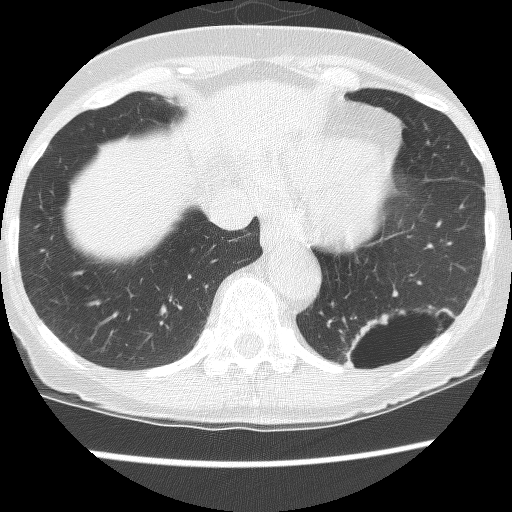
Axial slice from a low-dose chest CT screening exam, third annual screen, lung window (W 1500 / L -600 HU), 2.5 mm slice thickness, 120 kVp, 512 × 512 image matrix. Female, age 61 years at enrolment. Current smoker at enrolment.
- Expert reader's lesion annotation, bounding box (x1, y1, x2, y2) in pixels: (334, 294, 442, 387).
- The screening reader recorded 2 non-calcified nodules or masses ≥4 mm on this exam (left lower lobe, left lower lobe); which of them this box marks is not recorded.